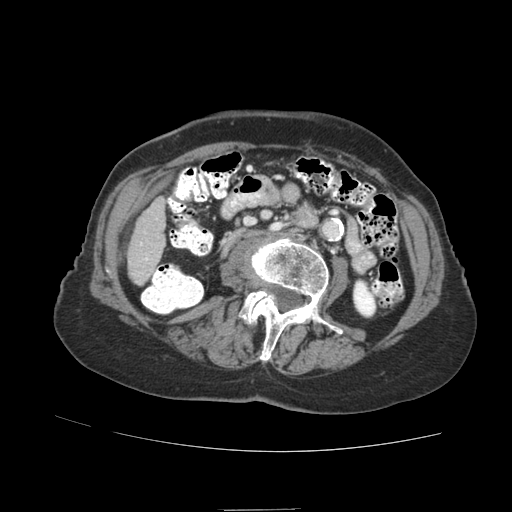
Contrast-enhanced abdominal CT (liver protocol), one axial slice; slice 15 of 89 in the series (ordered by position); reconstruction kernel STANDARD; 140 kVp; soft-tissue window (W 400 / L 40 HU); 2.5 mm slice thickness; 512 × 512 image matrix, field of view 360 × 360 mm. Case-level facts recorded for this patient, not image findings: diagnosis: hepatocellular carcinoma (patient treated with transarterial chemoembolisation; whether this scan precedes or follows treatment is not stated here); TNM stage (as recorded): Stage-II; Child-Pugh class: A.
Outlined on this slice (semi-automatic segmentation, software-assisted and operator-edited):
- liver parenchyma outside the tumour (the mass and vessels are separate outlines, so this box may not span the whole liver): box from (x=128, y=196) to (x=166, y=286) px
- liver vessels: (x=140, y=243)–(x=148, y=260)